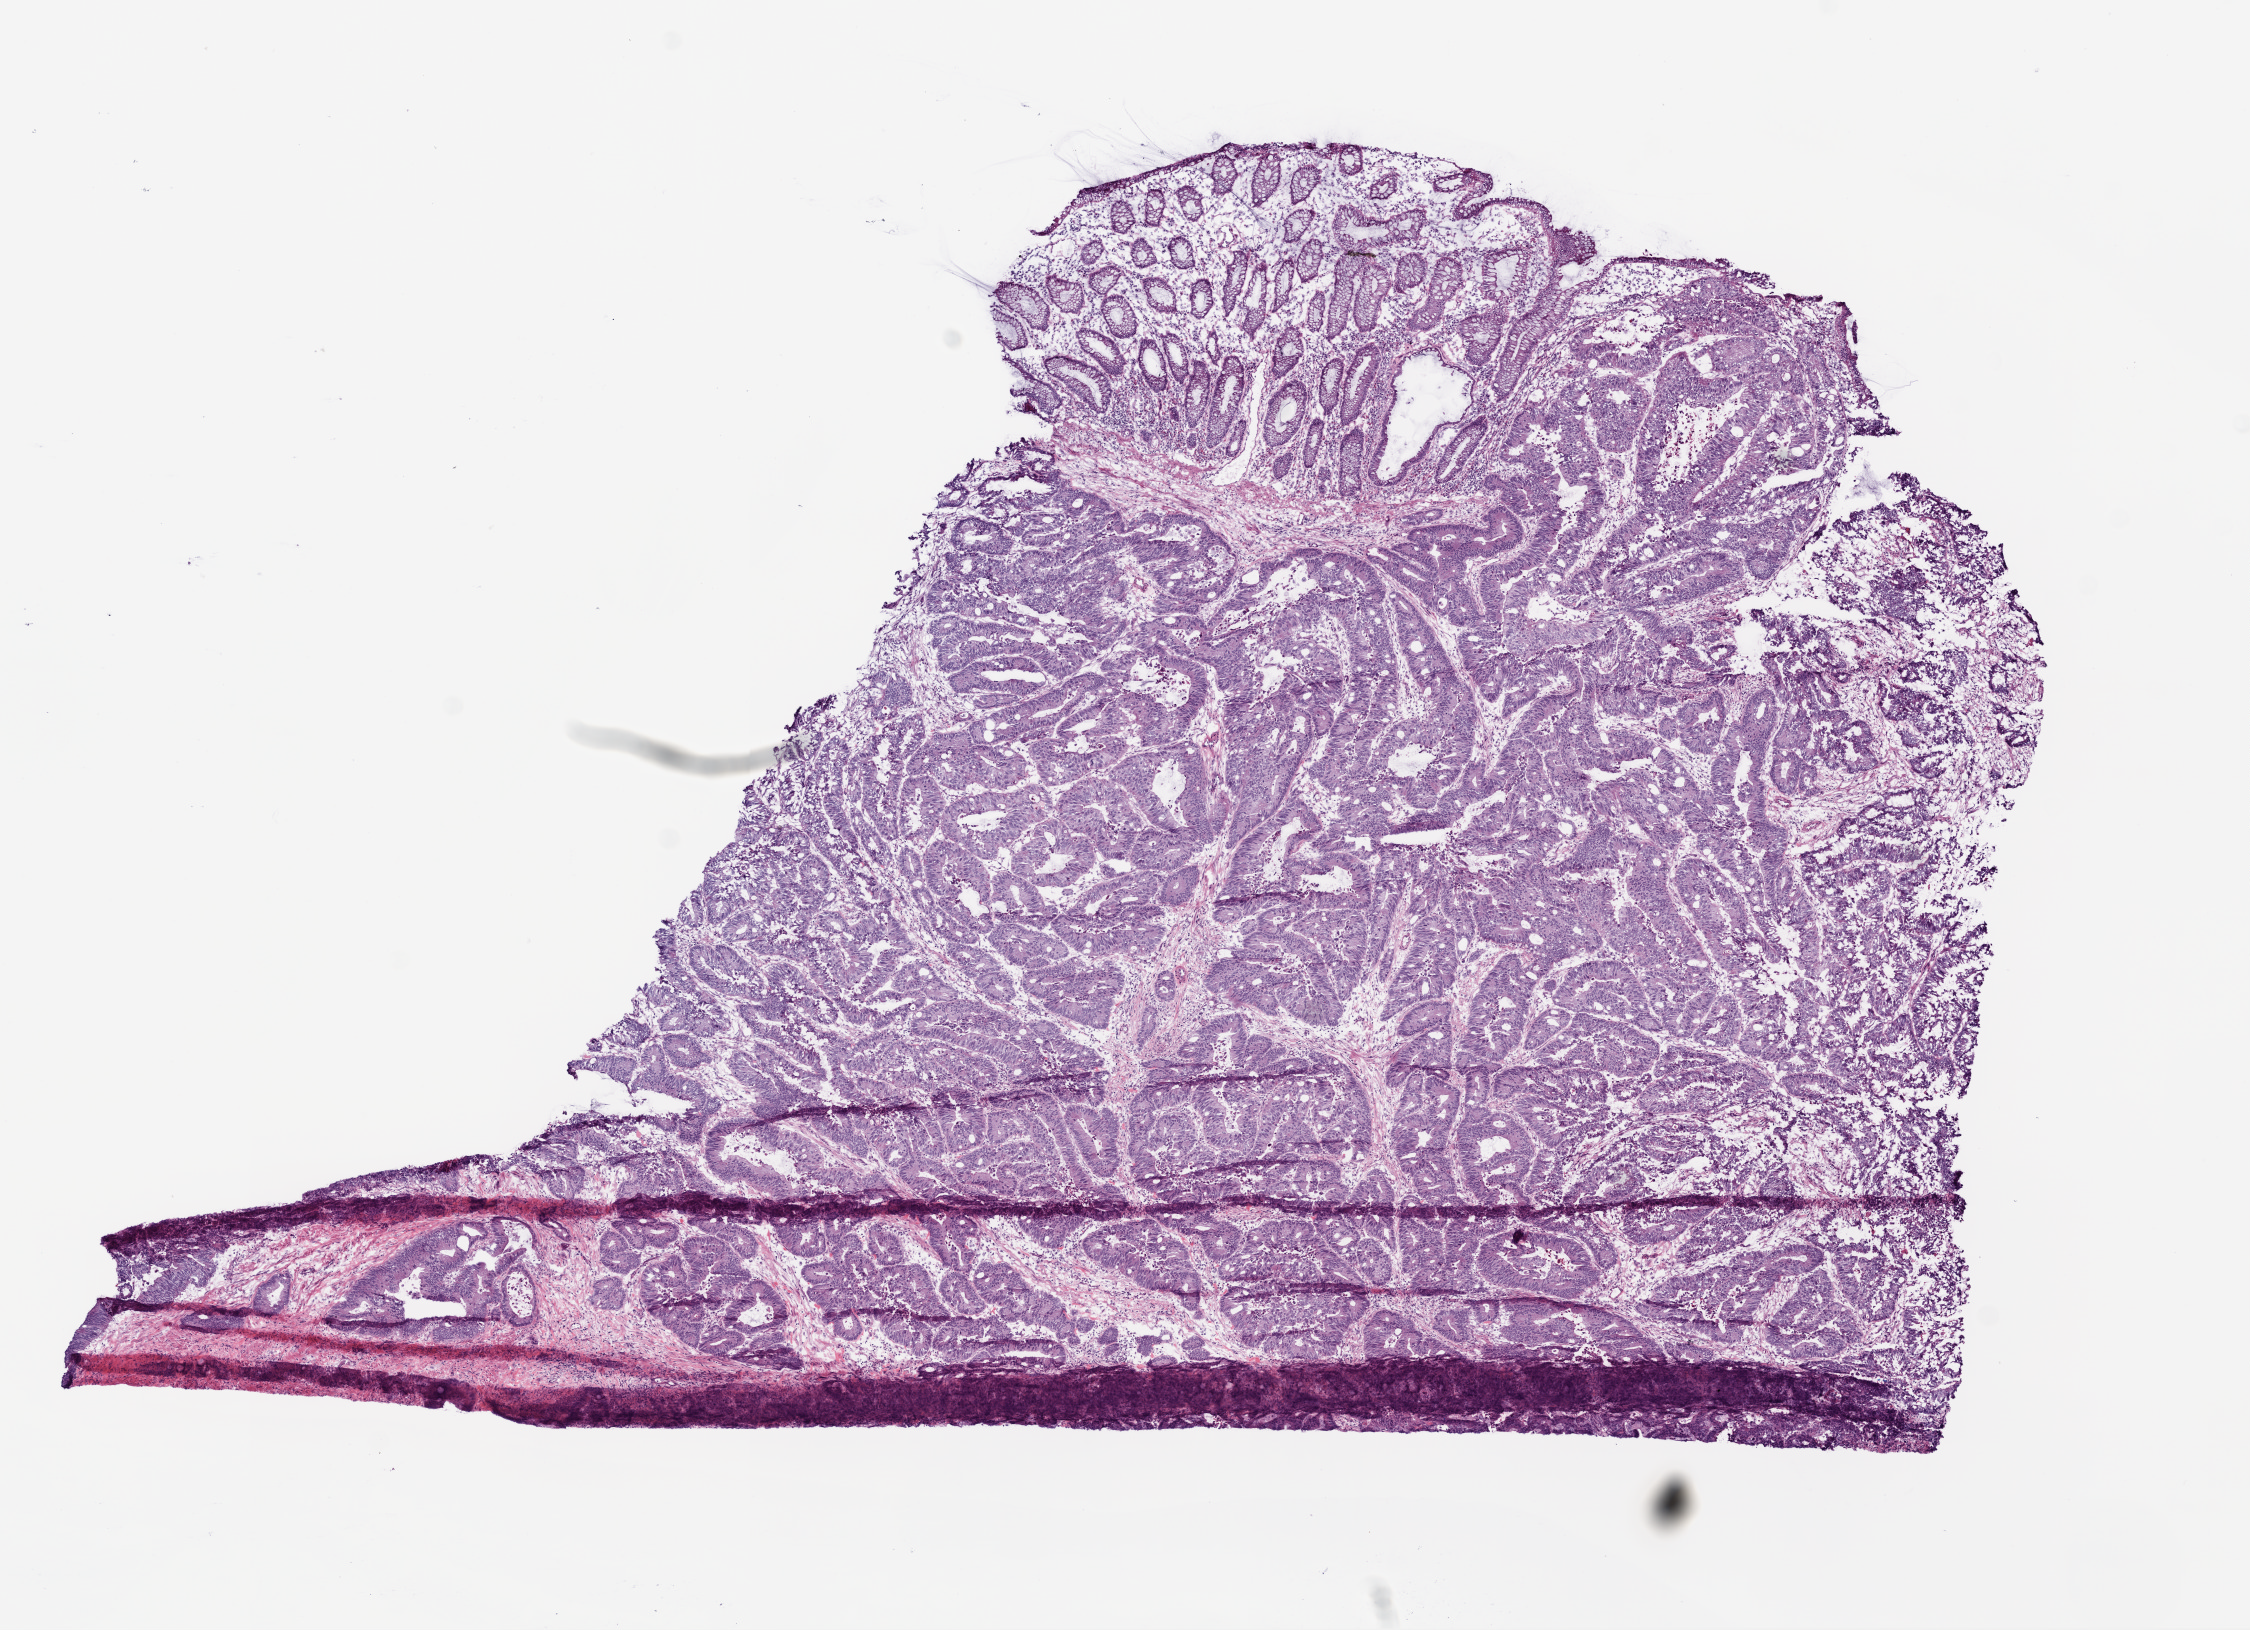
Whole-slide histology image, H&E, shown as a low-resolution overview of the whole scanned area (about 9.0 x 6.5 mm, from a 20x scan); frozen section; rectum, primary tumour sample. Female patient; age at initial diagnosis 69 years. Composition of this section per pathologist review: tumour cells 79%, tumour nuclei 80%, normal cells 8%, stromal cells 8%, necrosis 5%.
* AJCC pathologic stage: IIIB (6th edition)
* histologic diagnosis: Adenocarcinoma, NOS (rectosigmoid junction)
* lymph nodes positive (case pathology): 3 of 35 examined